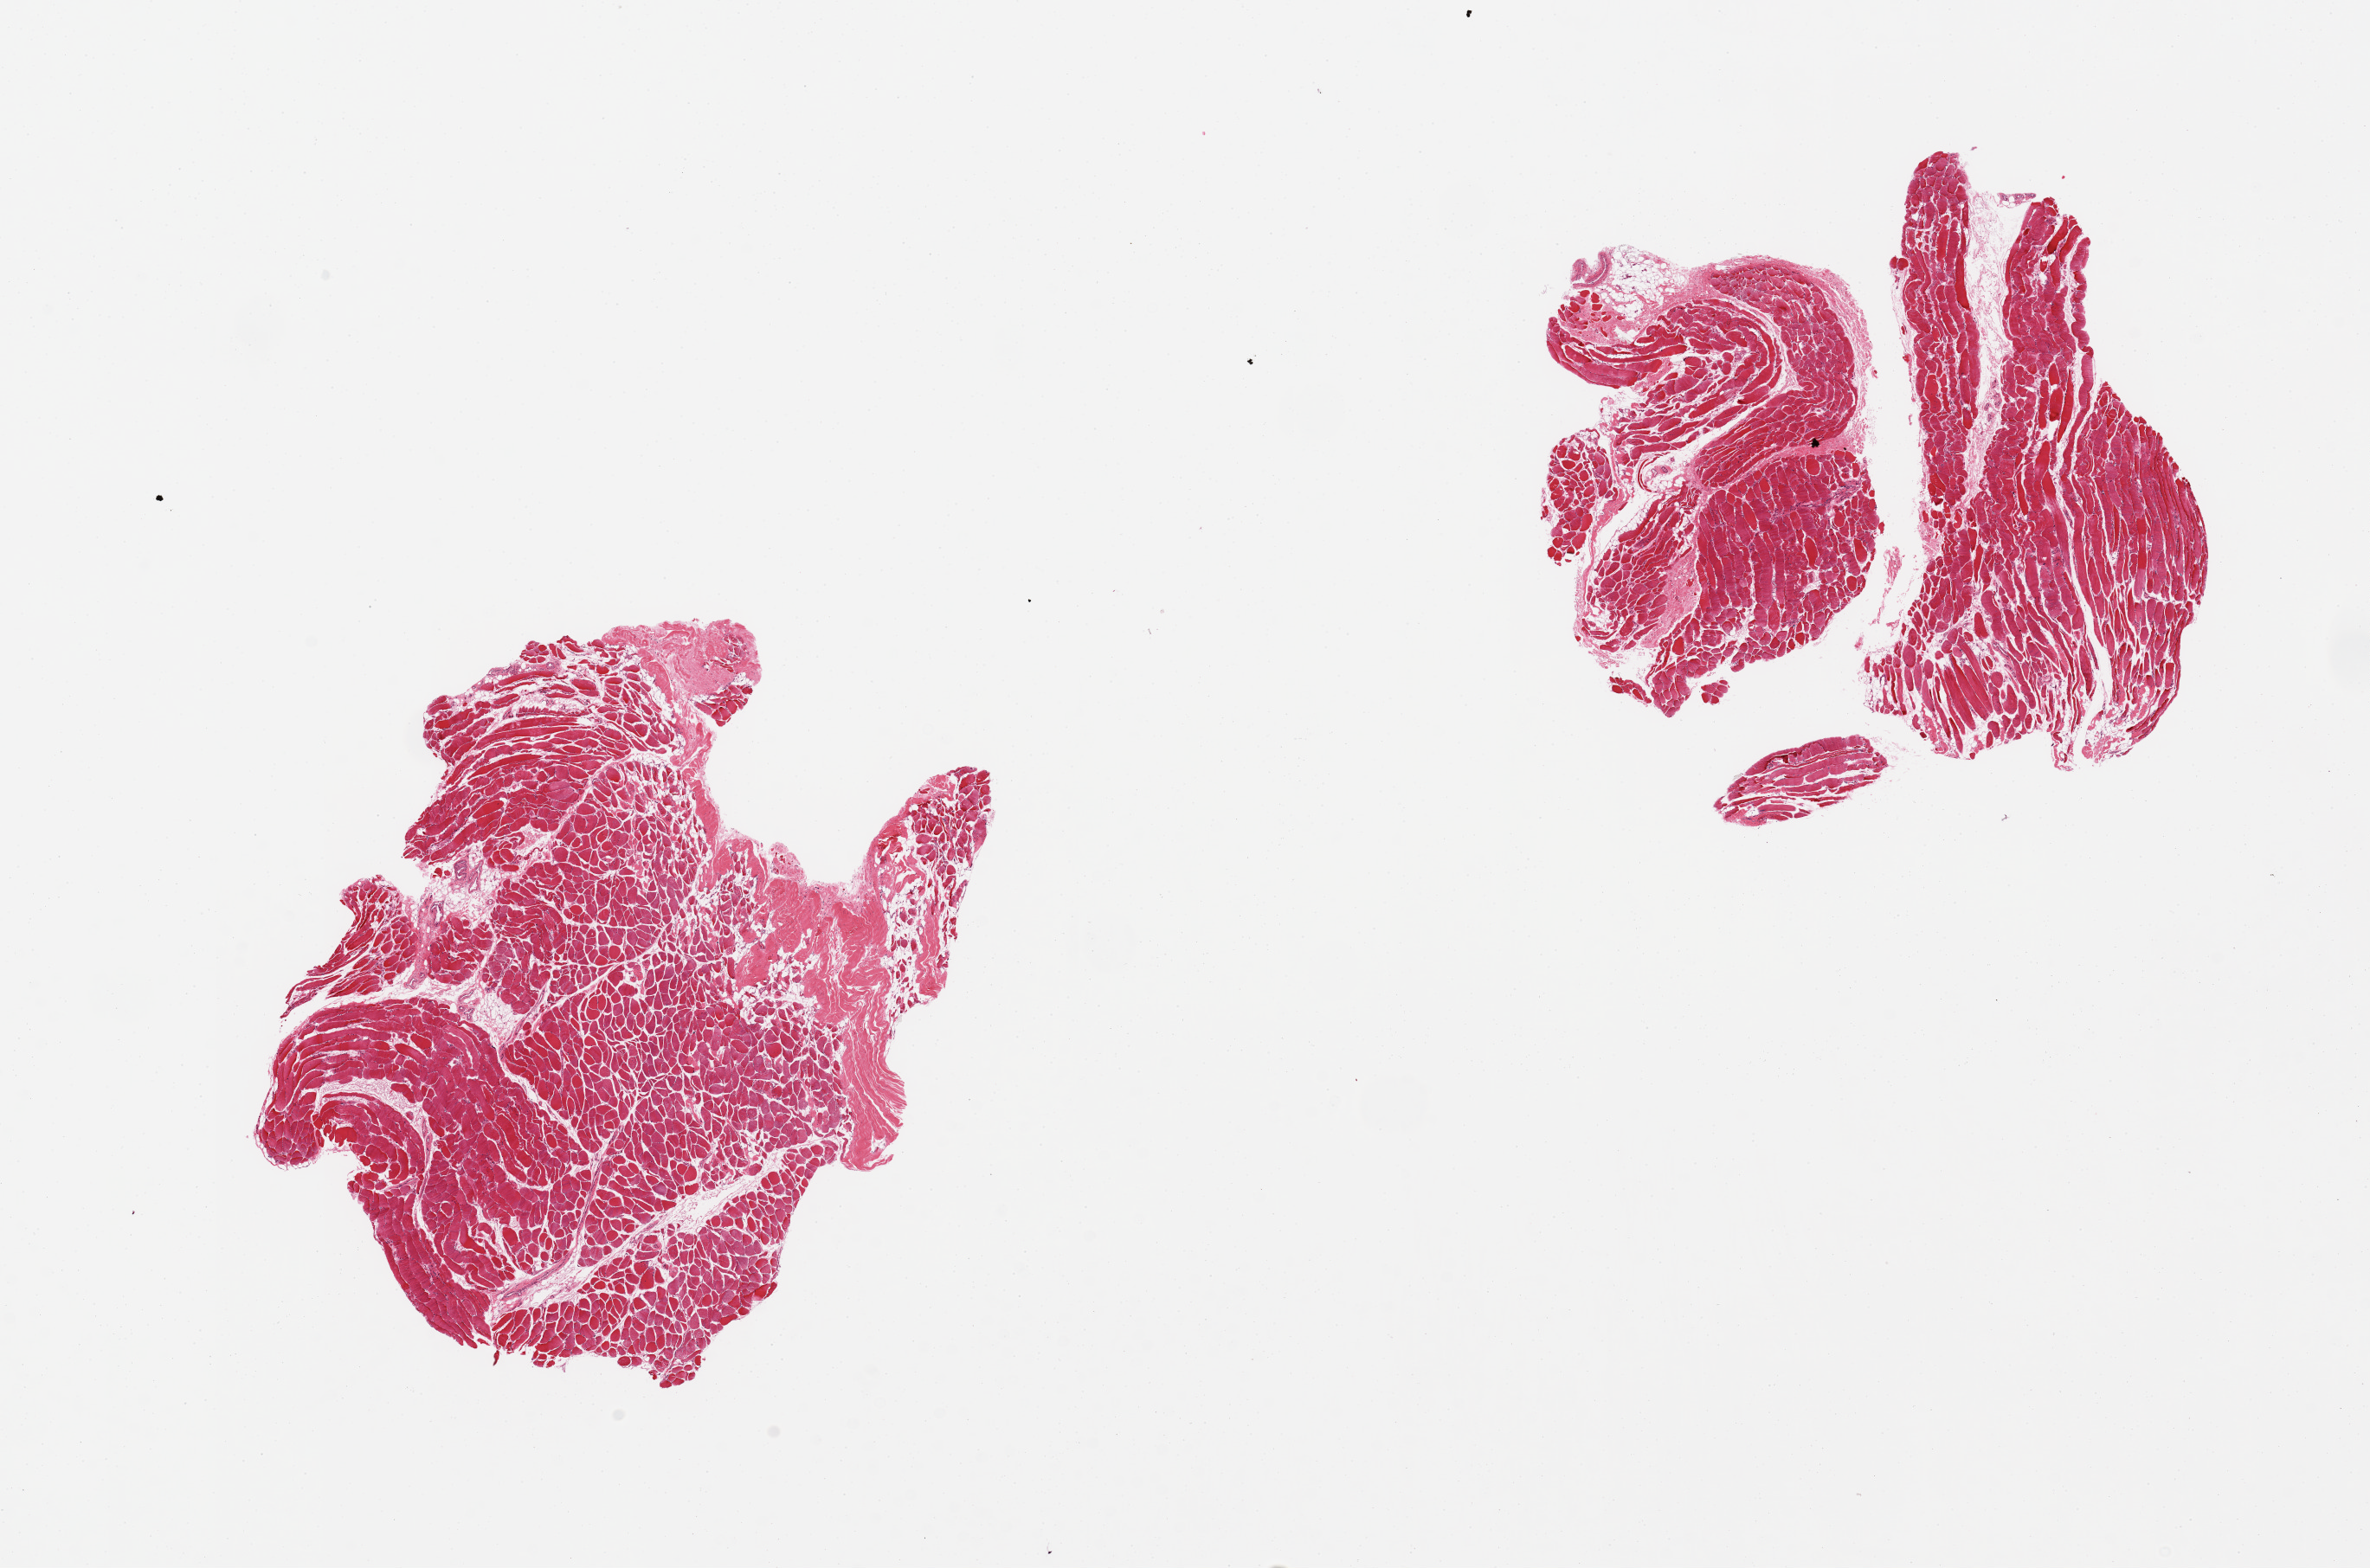
Whole-slide image, haematoxylin and eosin stain, shown as a low-resolution overview of the whole scanned area (about 21.7 x 14.3 mm, slide scanned at 20x); PAXgene-fixed, paraffin-embedded tissue; section of skeletal muscle (target tissue); donor tissue sample. Donor sex: female.
• pathologist's review note for this sample: 2 pieces, !5% fibrous connective tissue